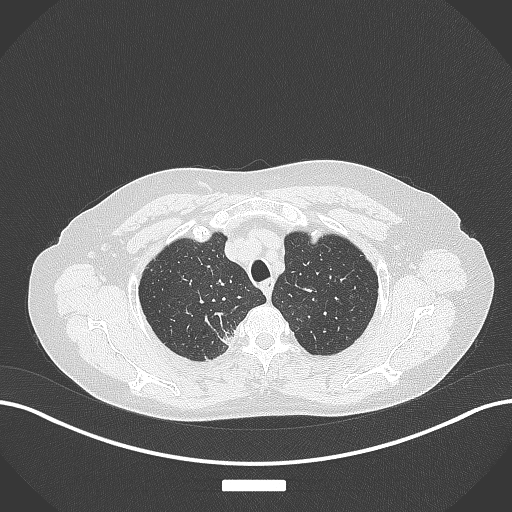
Chest CT, one axial slice. Position 327 of 357 along the scan axis. Reconstruction kernel B70f. 120 kVp. Lung window (W 1500 / L -600 HU). 512 × 512 image matrix, field of view 400 × 400 mm. Female patient, age 62 years. Case-level facts recorded for this patient, not image findings: clinical TNM (as recorded): T1c N1 M0.
Outlined on this slice (rectangle marked by the reading radiologist):
- lung tumour (recorded histology: squamous cell carcinoma): bounding box <218,332,235,350> (left, top, right, bottom; pixels)